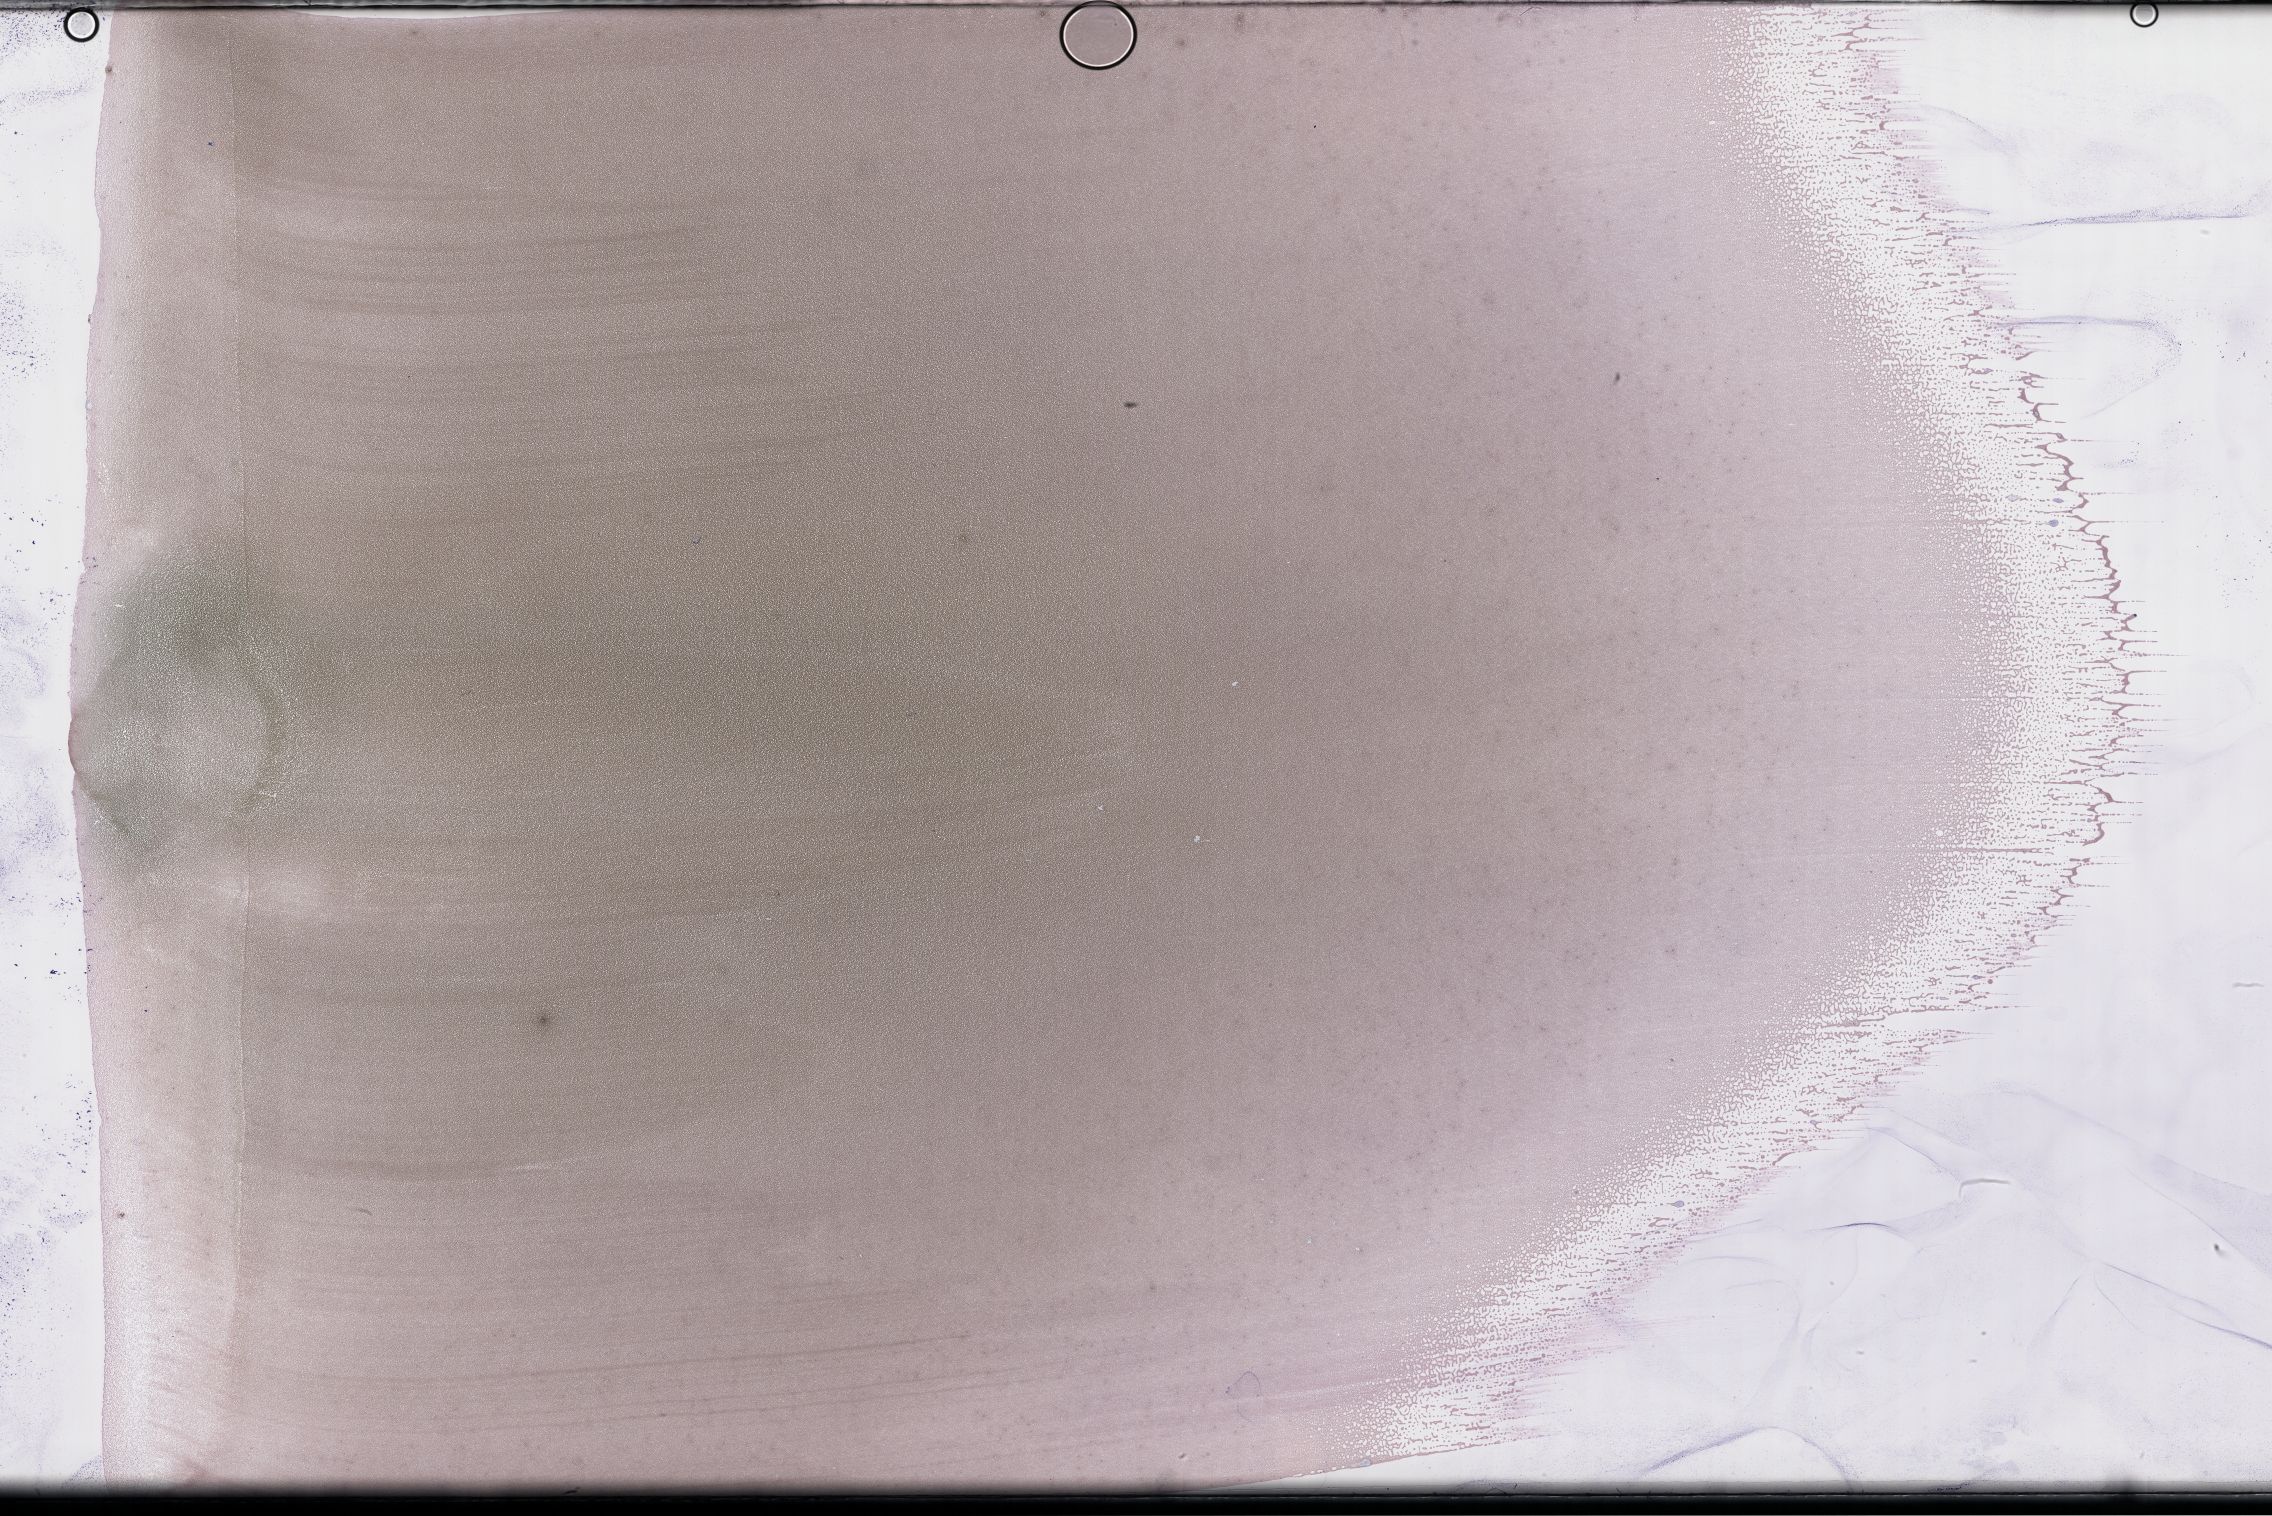
Wright-Giemsa-stained whole blood smear, whole-slide image, low-resolution overview of the scanned area, about 36.7 x 24.5 mm, specimen time point: collected on treatment. Patient: male.
From a patient with: Plasma Cell Myeloma.